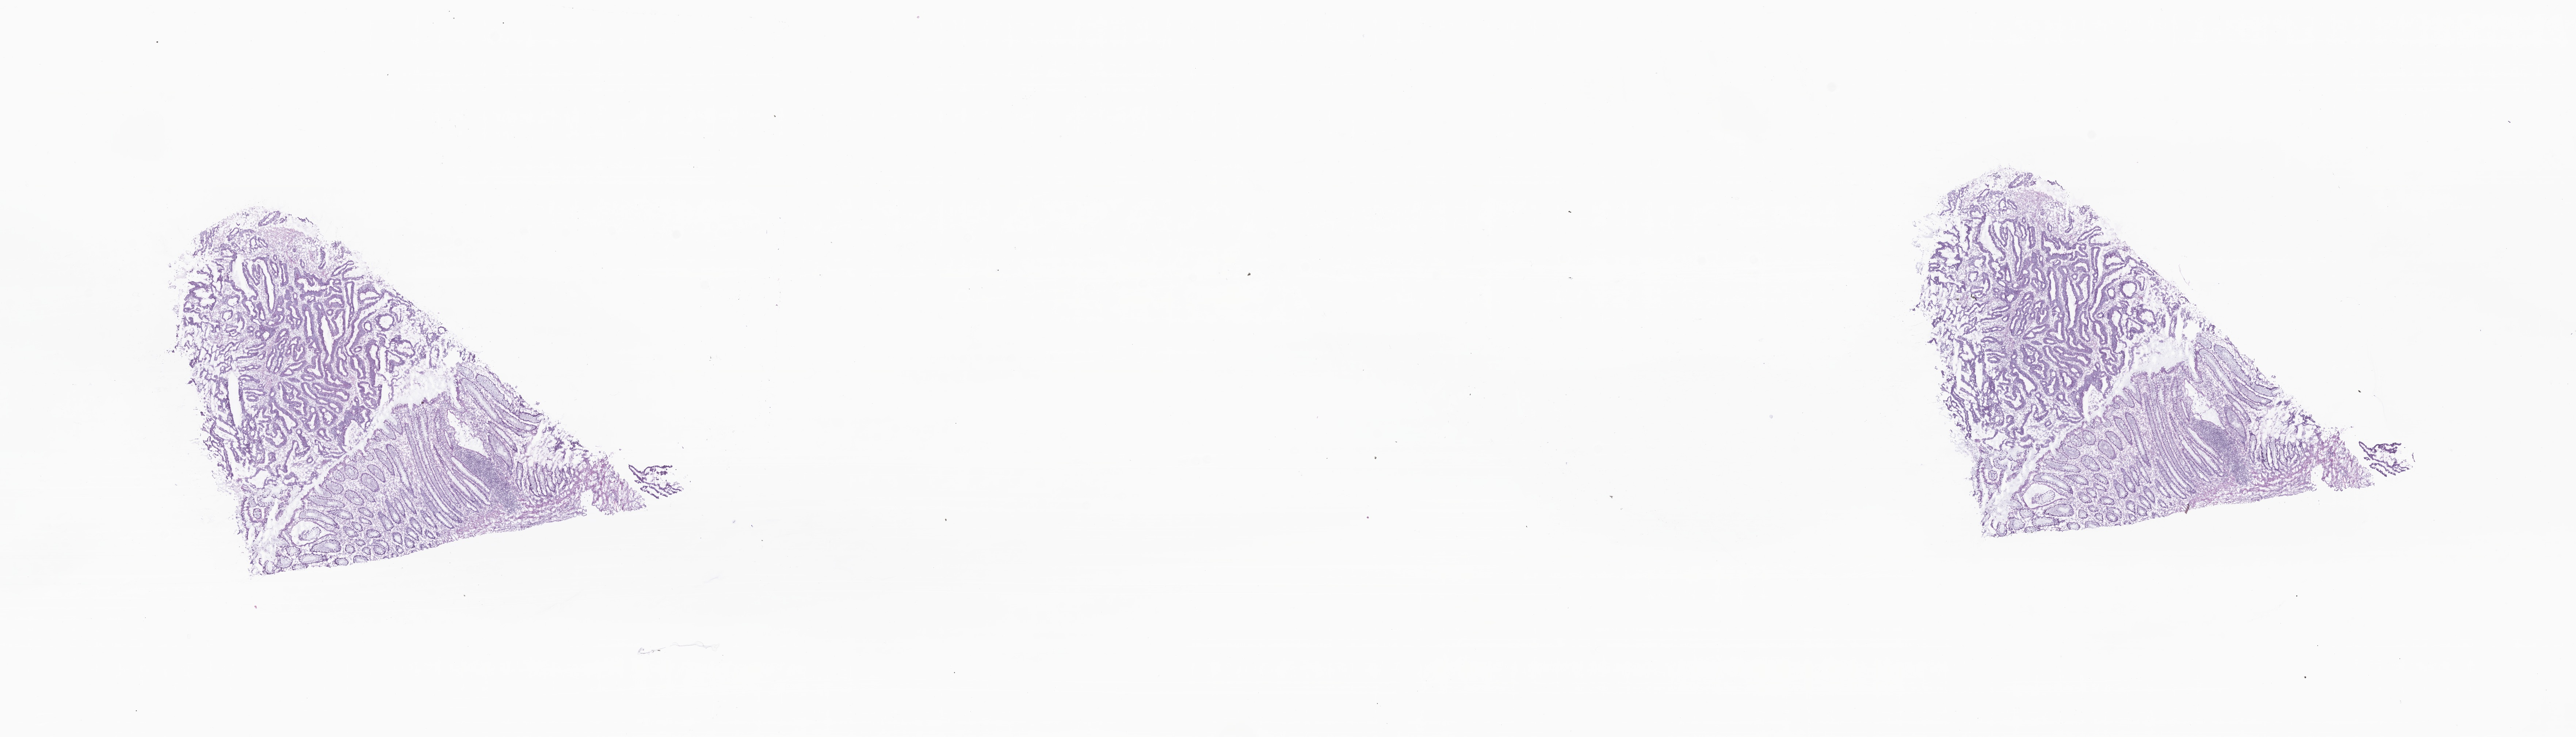
H&E whole-slide image, whole scanned area (about 29.7 x 8.5 mm) shown as a low-resolution overview. Cryosection. Specimen: primary tumor. Anatomic site: sigmoid colon. Male, age 60 years at initial diagnosis. Pathologist review of this section (percent, as recorded): tumor cells 37%, tumor nuclei 52%, stromal cells 27%, necrosis 2%, normal cells 34%. Inflammatory infiltration, as recorded: lymphocyte infiltration 20%, monocyte infiltration 2%, neutrophil infiltration 0%.
• histologic diagnosis: Adenocarcinoma, NOS
• section: bottom of the tissue portion